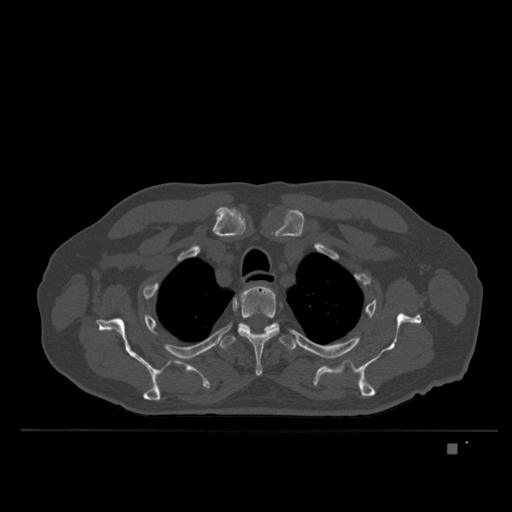
CT including the spine, one axial slice; slice 298 of 435 in the series (ordered by position); bone window (W 1800 / L 400 HU); 1.5 mm slice thickness; 512 × 512 image matrix. Patient: male, 73 years. From the clinical record (not read from this slice): primary cancer: skin.
Structures marked on this image (semi-automatically segmented with operator editing):
- T2 vertebra: box from (x=242, y=290) to (x=244, y=293) px
- T3 vertebra: (x=237, y=284)–(x=280, y=376)
- T4 vertebra: (x=219, y=324)–(x=297, y=351)